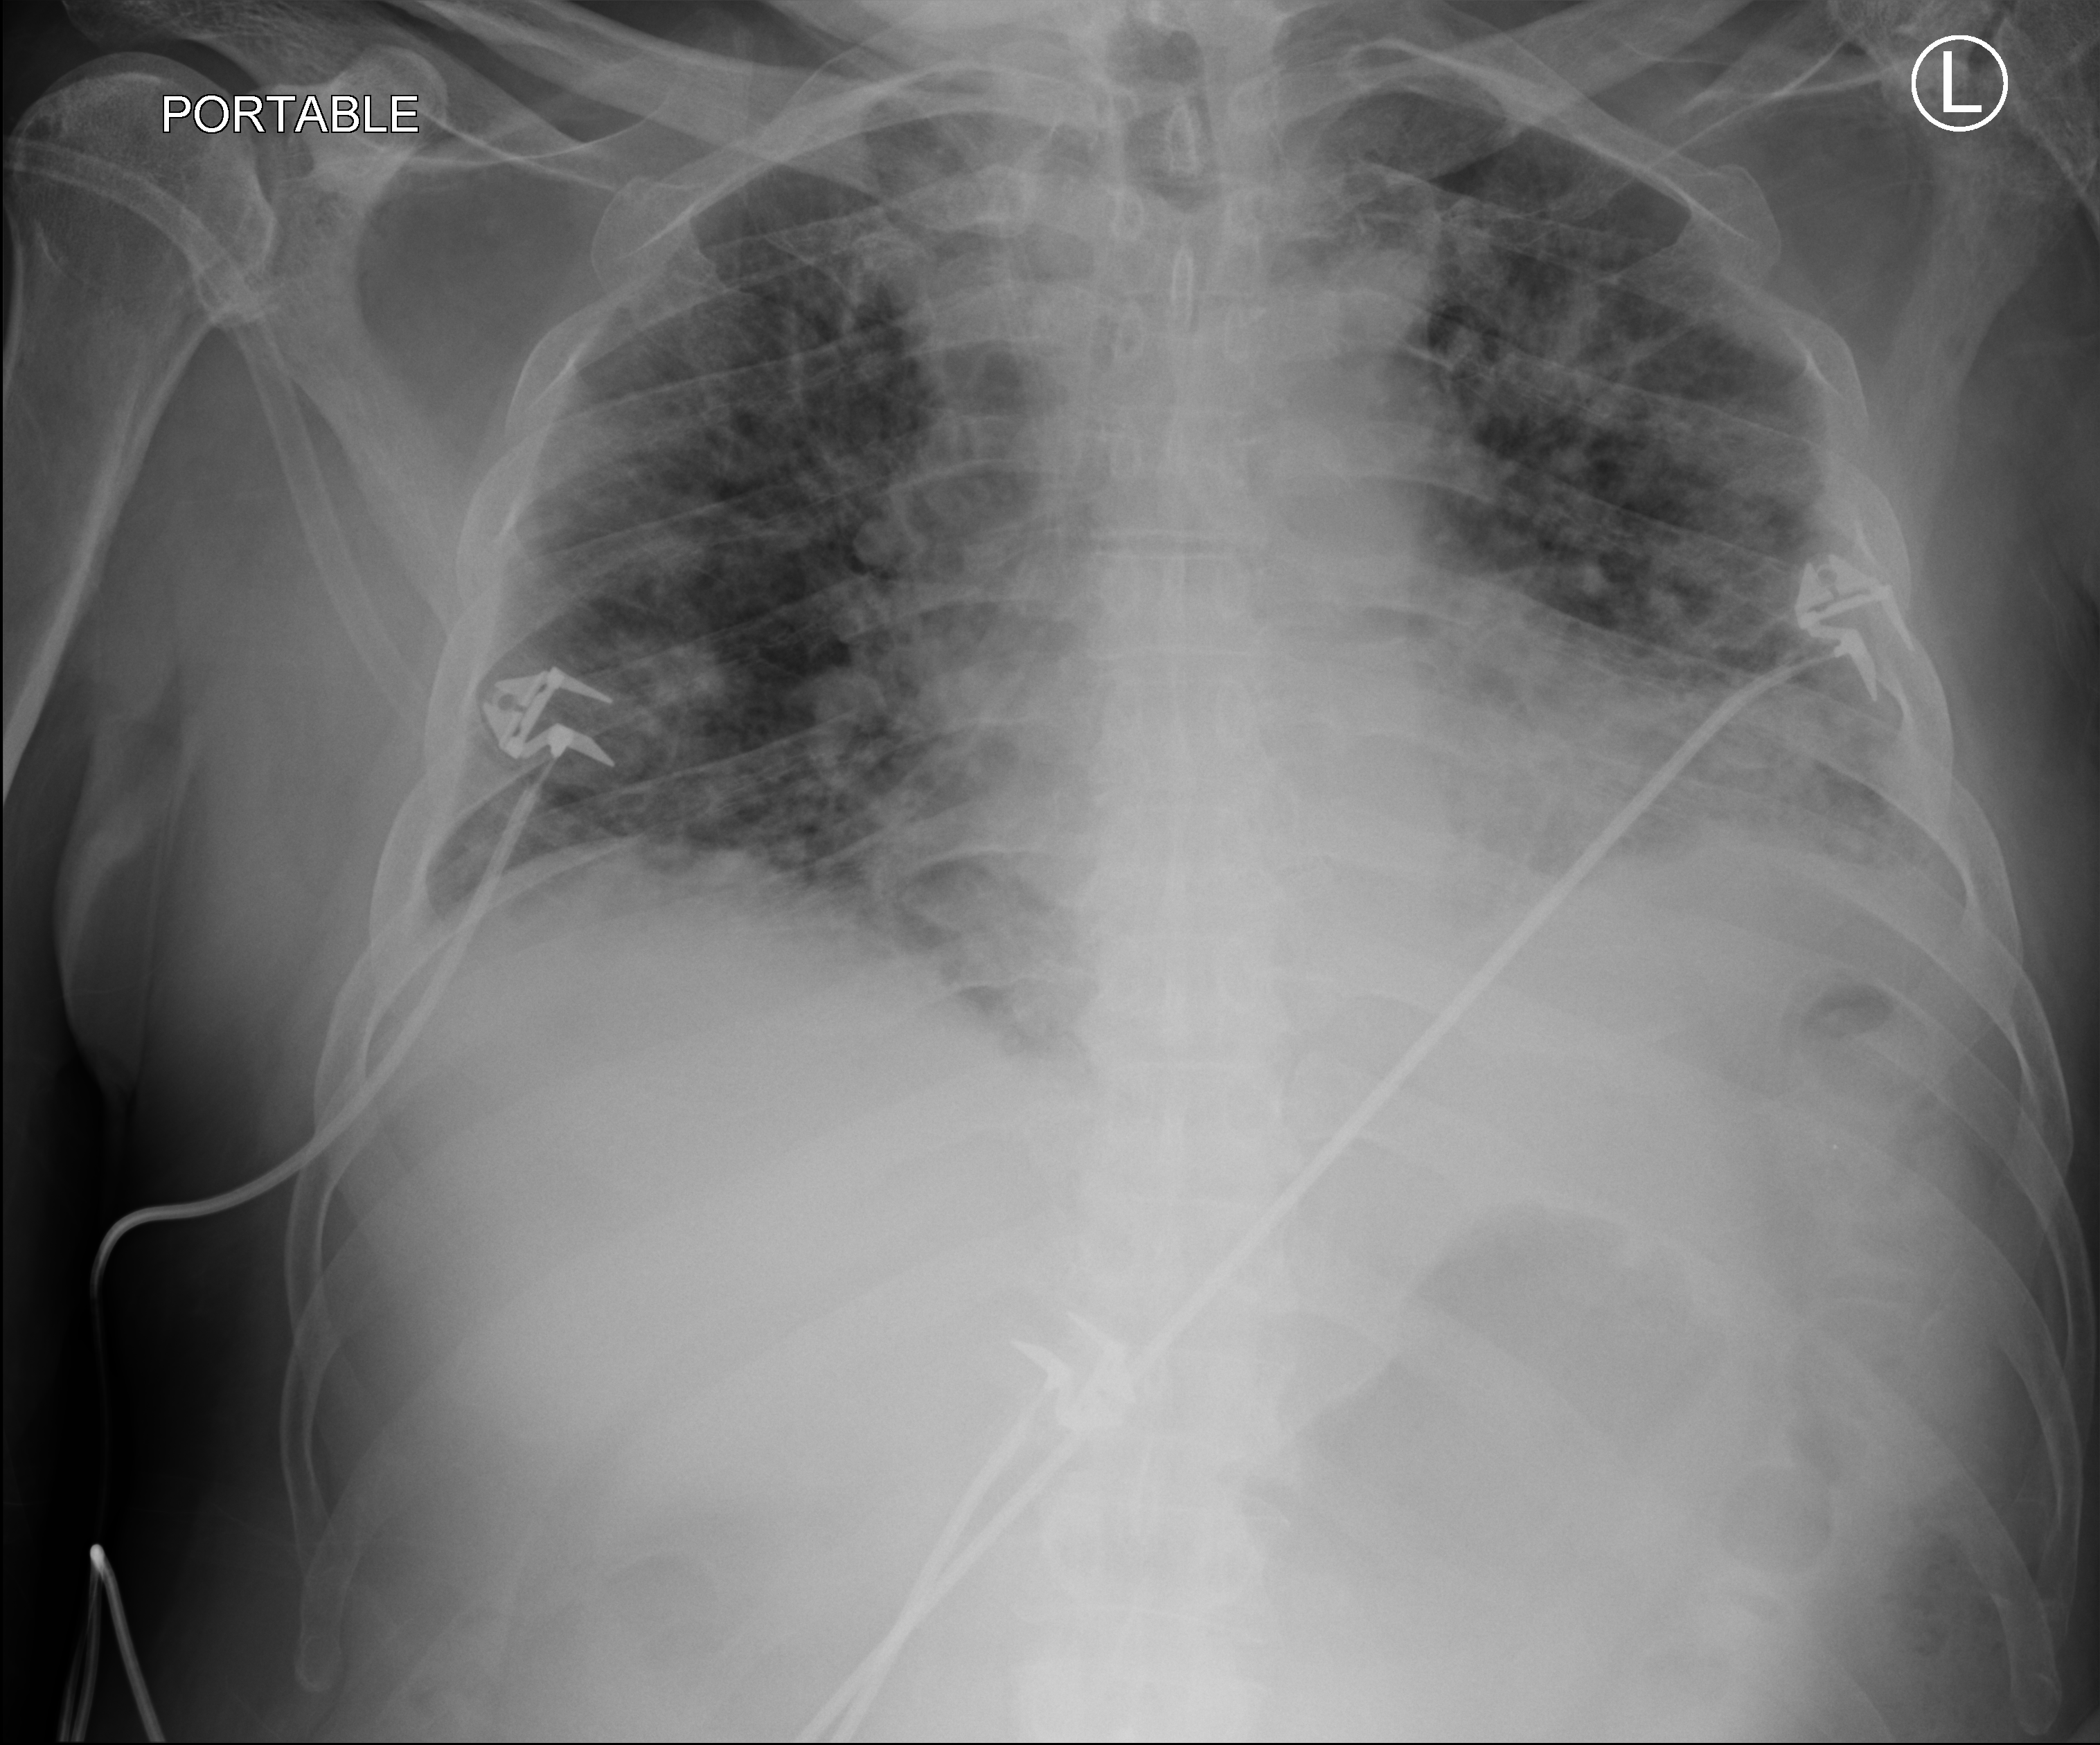
Portable chest radiograph; anteroposterior (AP) projection. Patient hospitalised with COVID-19; male, aged 60–74 years.
Admission-level facts for this patient (not findings on this image; timing relative to this image not recorded): admitted to intensive care during this hospital stay: no; length of hospital stay: 27 days; hypertension (admission record): yes.